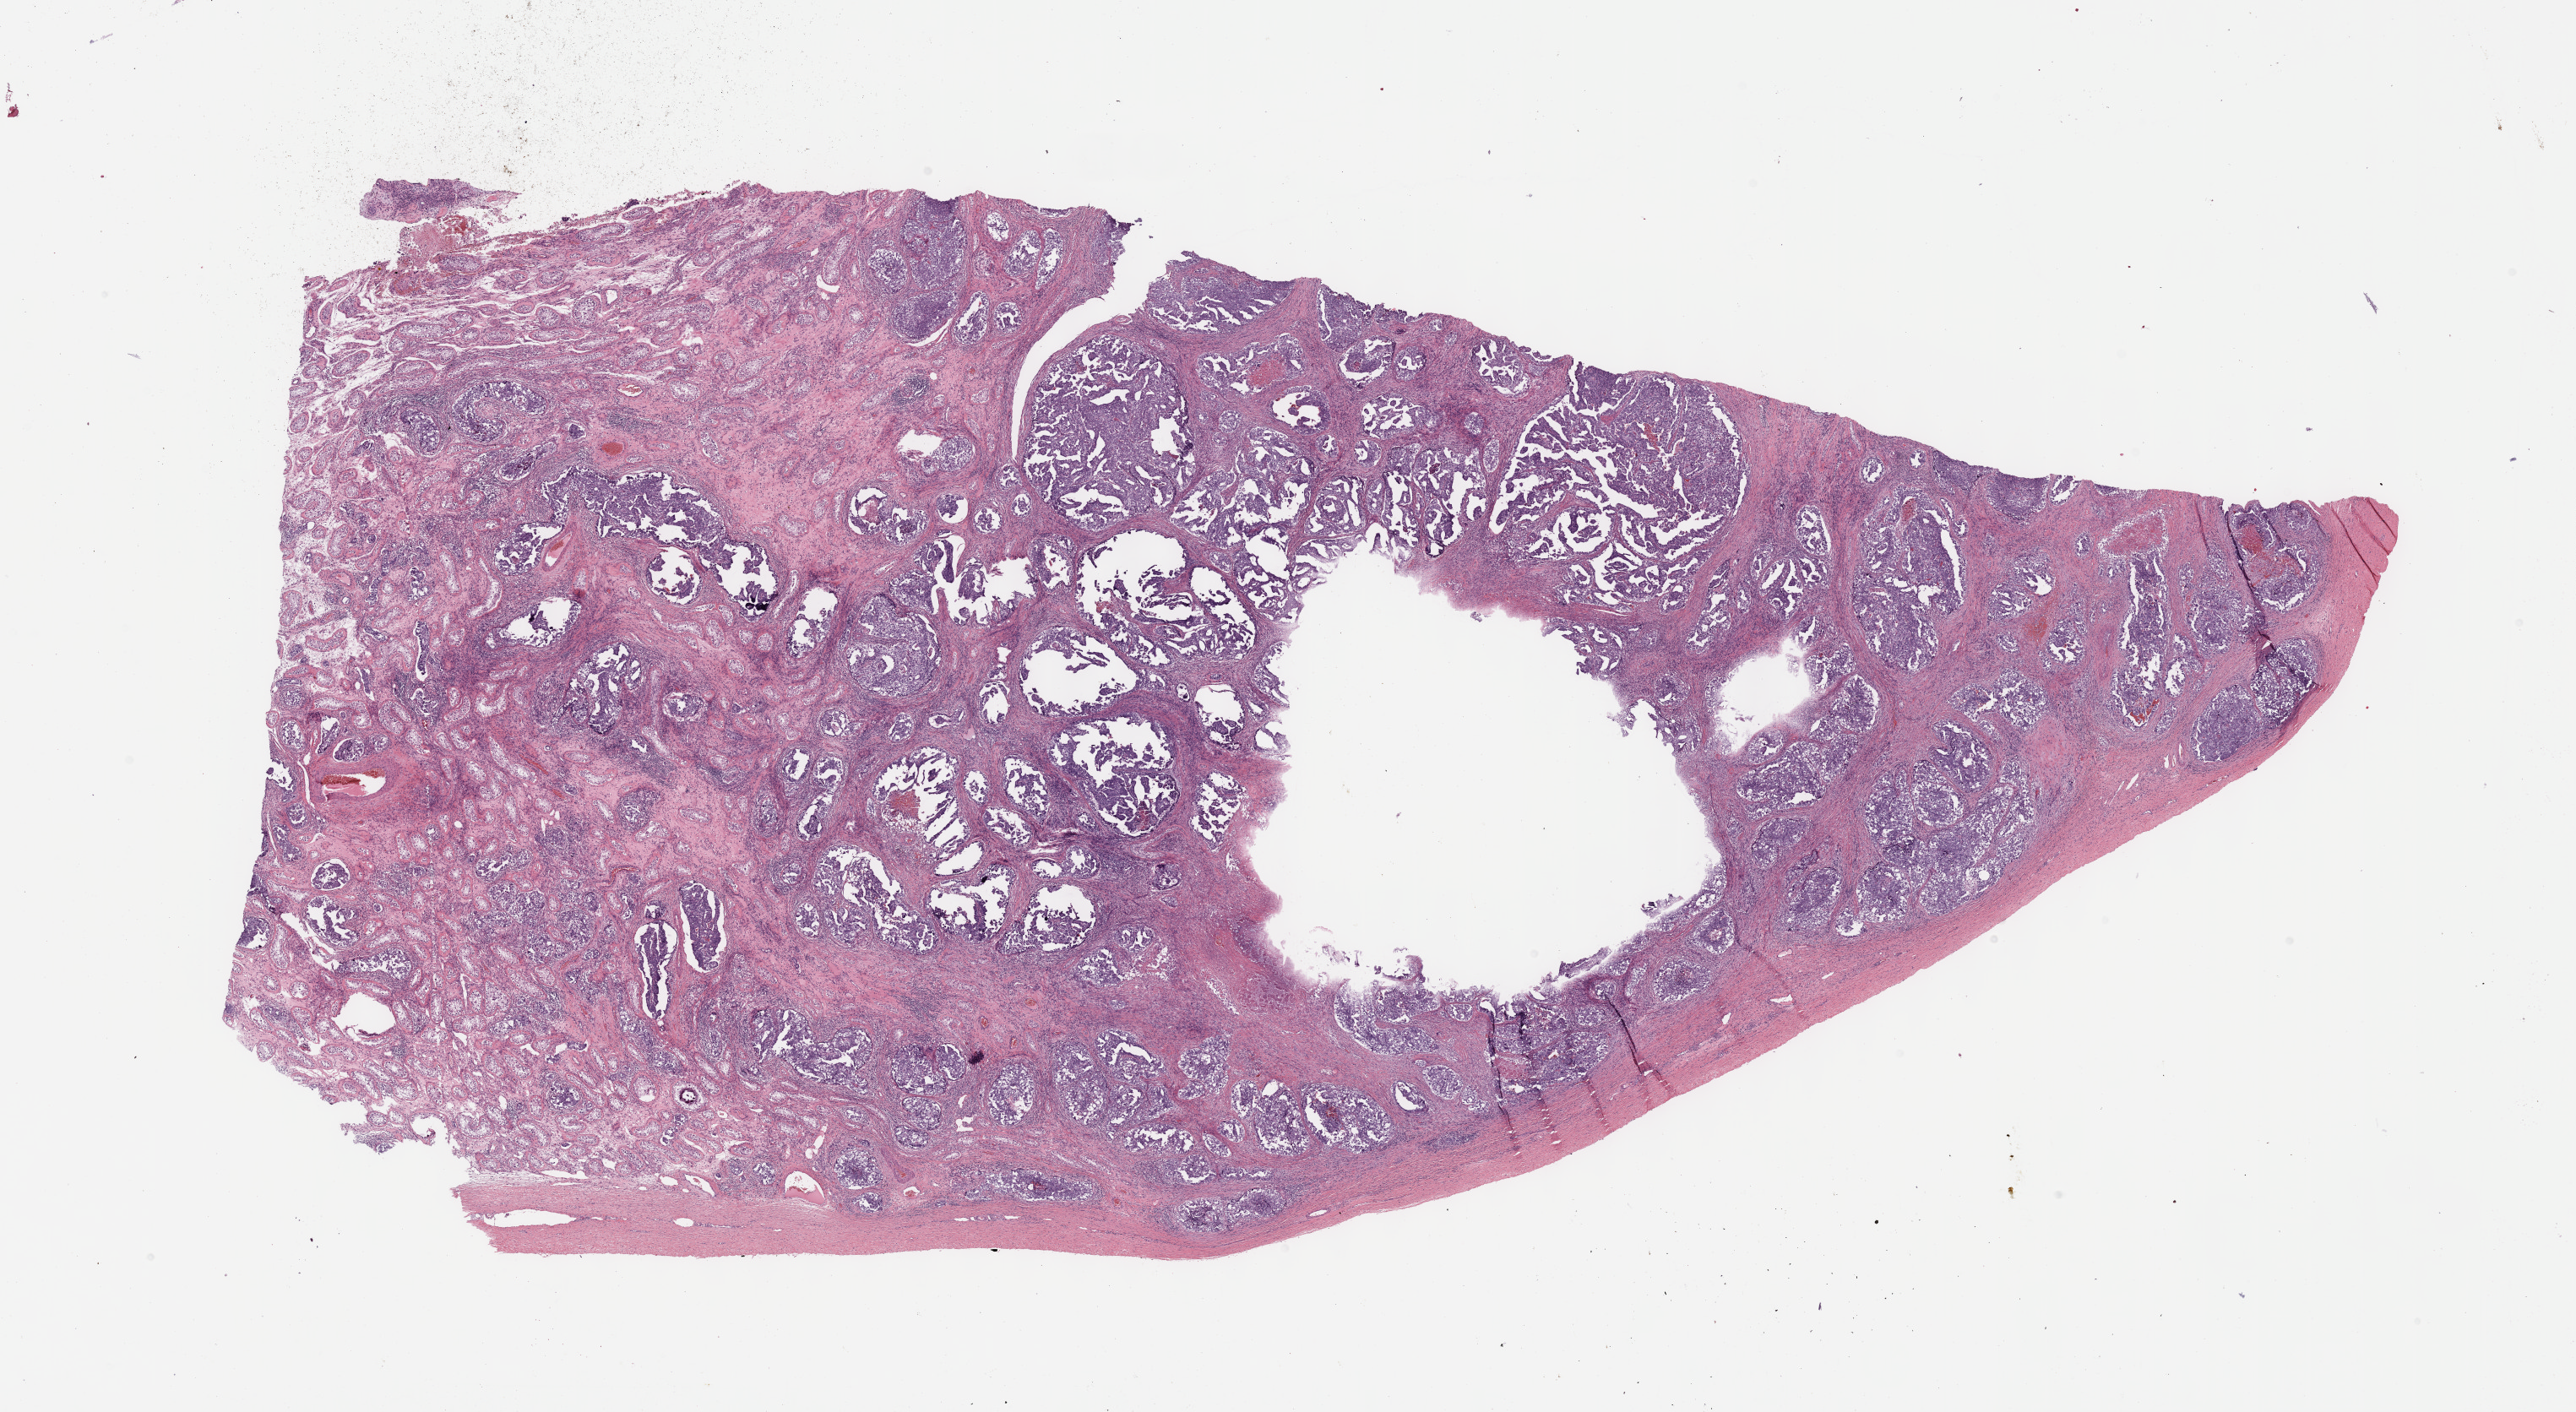
Digitized Hematoxylin and eosin (H&E) stained tissue section (whole slide) — shown as a low-resolution overview of the whole scanned area (about 24.7 x 13.5 mm, from a 40x scan), formalin-fixed paraffin-embedded (FFPE) diagnostic section, testis, primary tumour sample. Male, age 23 years at initial diagnosis.
• histologic diagnosis: Embryonal carcinoma, NOS
• AJCC pathologic stage: IIIC